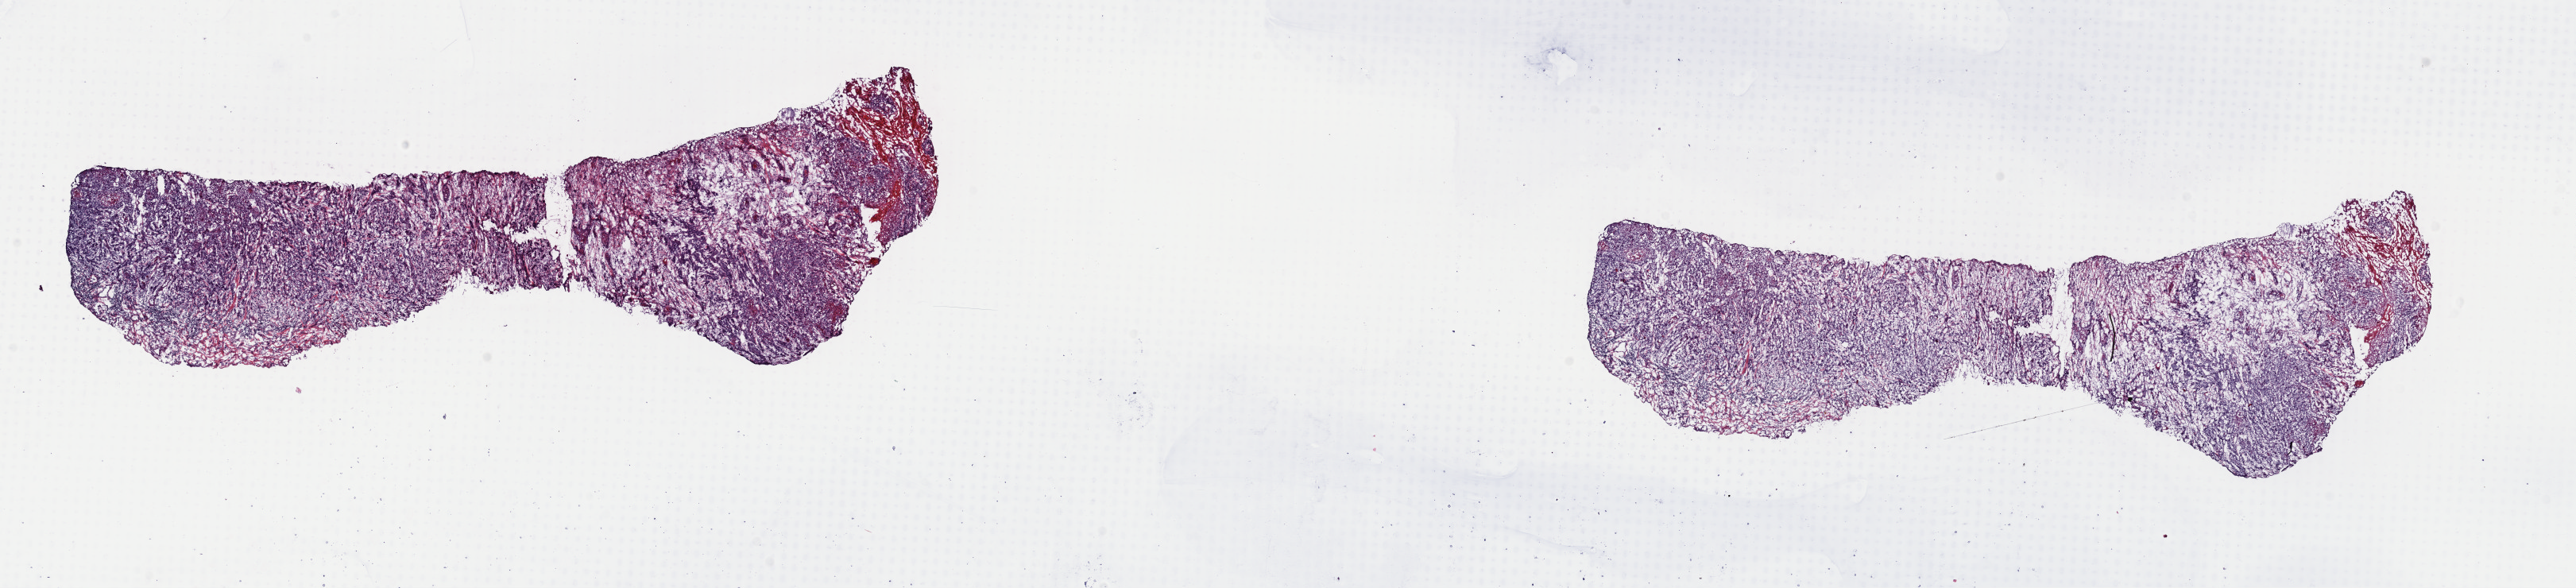
Digitized H&E-stained tissue section (whole slide) — shown as a low-resolution overview of the whole scanned area (about 25.6 x 5.8 mm), frozen section from the top of the tissue portion, head and neck, primary tumour sample. Patient: male, age at initial diagnosis 88 years. Histologic grade: G3 (poorly differentiated). Slide review estimates, as recorded: tumour cells 80%, tumour nuclei 90%, normal cells 0%, stromal cells 20%, necrosis 0%. Inflammatory infiltration, as recorded: lymphocyte infiltration 0%, monocyte infiltration 0%, neutrophil infiltration 0%.
* AJCC pathologic stage: III (7th edition)
* pathologic diagnosis: Squamous cell carcinoma, NOS
* TNM: T3 N1 M0